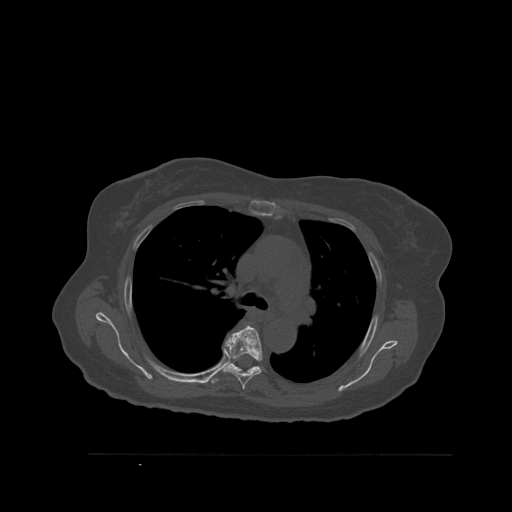
CT including the spine, one axial slice; position 391 of 527 along the scan axis; bone window (W 1800 / L 400 HU); 512 × 512 image matrix, field of view 470 × 470 mm. Patient: female, 73 years. Case-level facts recorded for this patient, not image findings: primary cancer: breast; vertebrae with lytic lesions (as recorded): L2.
Outlined on this slice (semi-automatically segmented with operator editing):
- T5 vertebra: bounding box <222,325,263,390> (left, top, right, bottom; pixels)
- T6 vertebra: <211,334,262,385>